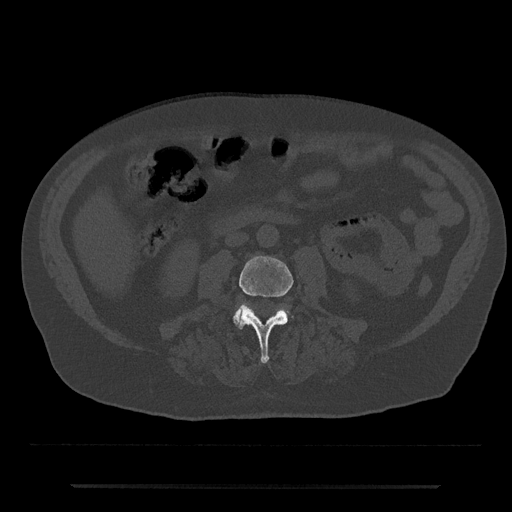
CT including the spine, one axial slice; position 397 of 797 along the scan axis; bone window (W 1800 / L 400 HU); 0.5 mm slice thickness; 512 × 512 image matrix, field of view 434 × 434 mm. Male patient, age 80 years. From the clinical record (not read from this slice): primary cancer: prostate; vertebrae with lytic lesions (as recorded): L1, T11.
Structures marked on this image (semi-automatically segmented with operator editing):
- L3 vertebra: bounding box <238,256,294,363> (left, top, right, bottom; pixels)
- L4 vertebra: <233,306,289,326>